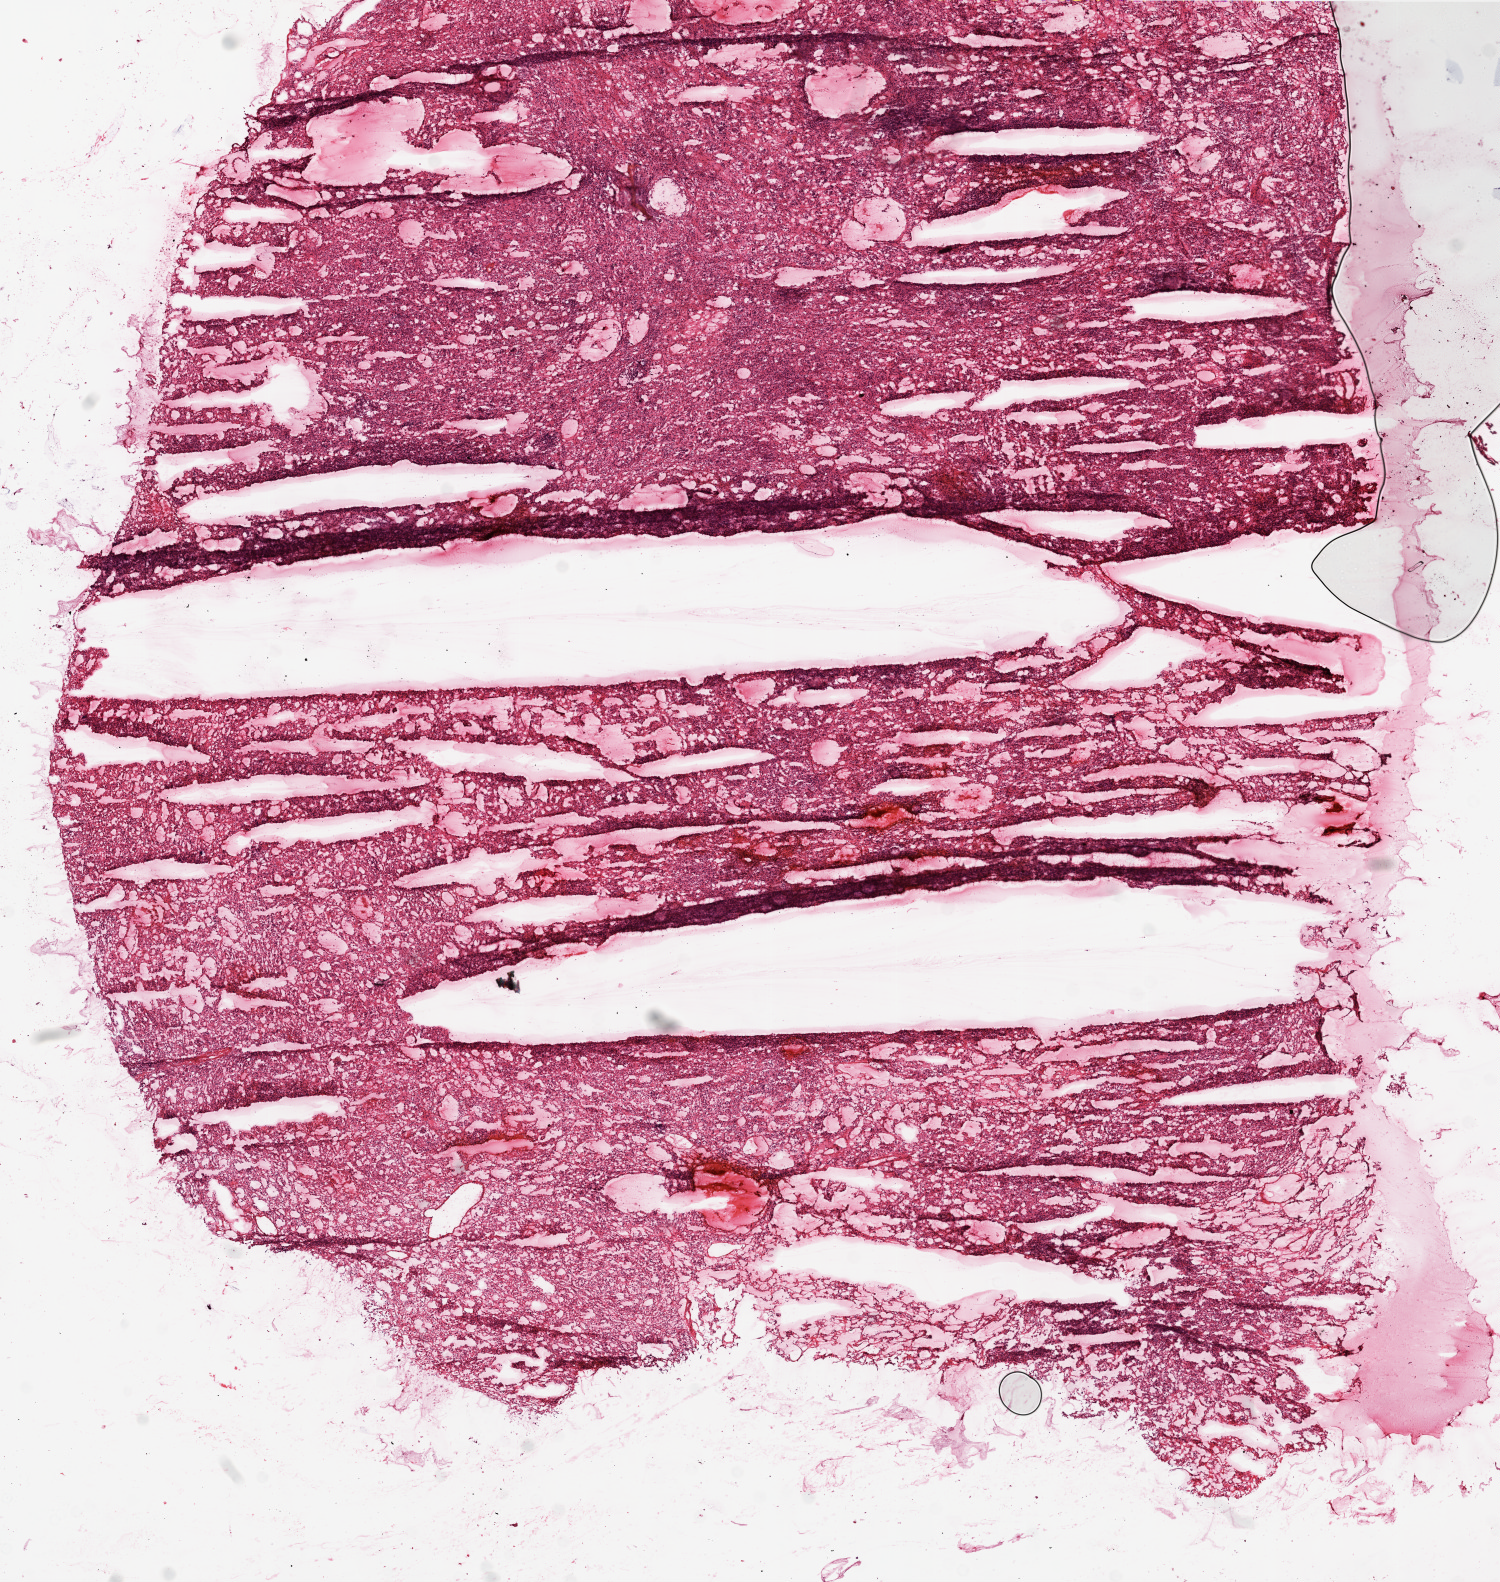
H&E-stained whole-slide image — low-resolution overview of the scanned area, about 12.0 x 12.7 mm (acquisition: 20x scan). Frozen section. Primary tumour sample from the kidney. Female patient; age at initial diagnosis 49 years. Histologic grade: G3 (poorly differentiated). Composition of this section per pathologist review: tumour cells 95%, tumour nuclei 85%, normal cells 0%, stromal cells 5%, necrosis 0%.
Pathologic diagnosis: Clear cell adenocarcinoma, NOS. Laterality: left. TNM: T1a N0 M0. AJCC pathologic stage: I.